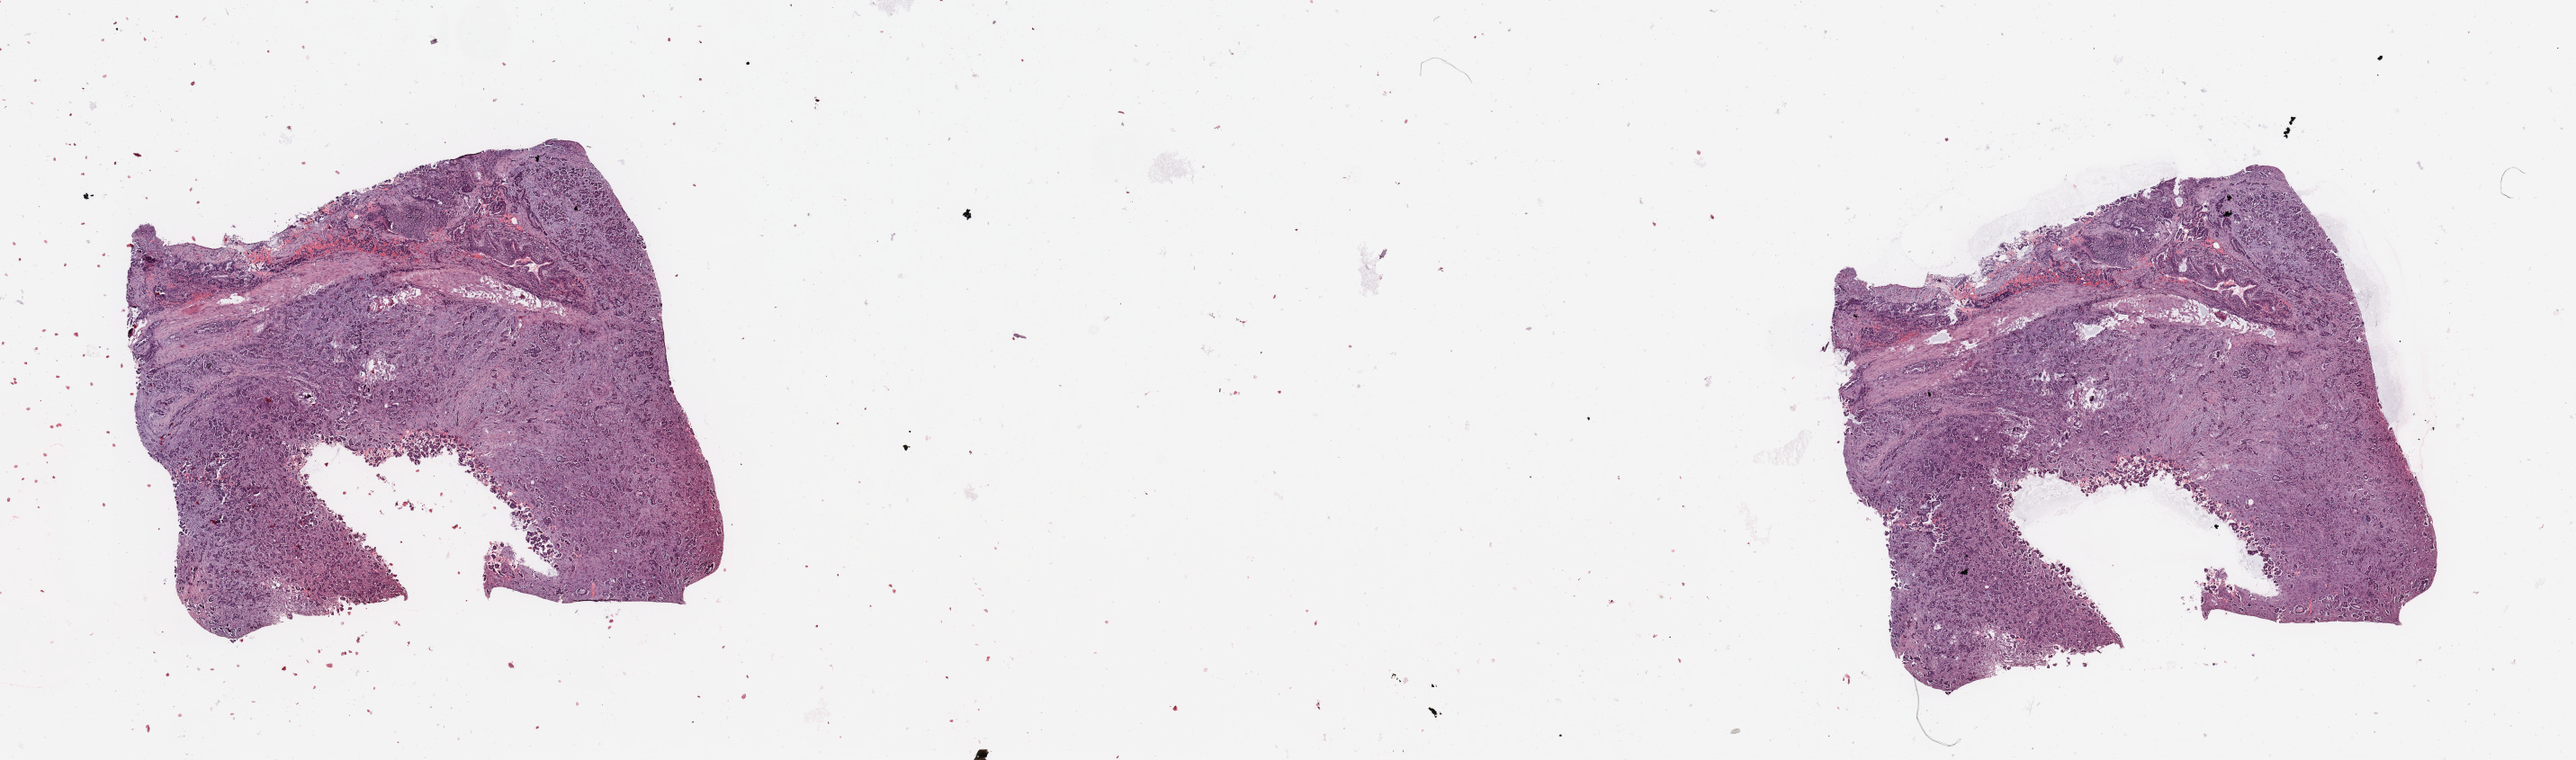
Hematoxylin and eosin (H&E) stained whole-slide image — shown as a low-resolution overview of the whole scanned area (about 22.6 x 6.7 mm). Tumour tissue sample, lung. 39-year-old male patient. Histologic grade: G2 (moderately differentiated).
• AJCC pathologic stage: IIIA
• histologic diagnosis: Adenocarcinoma, NOS